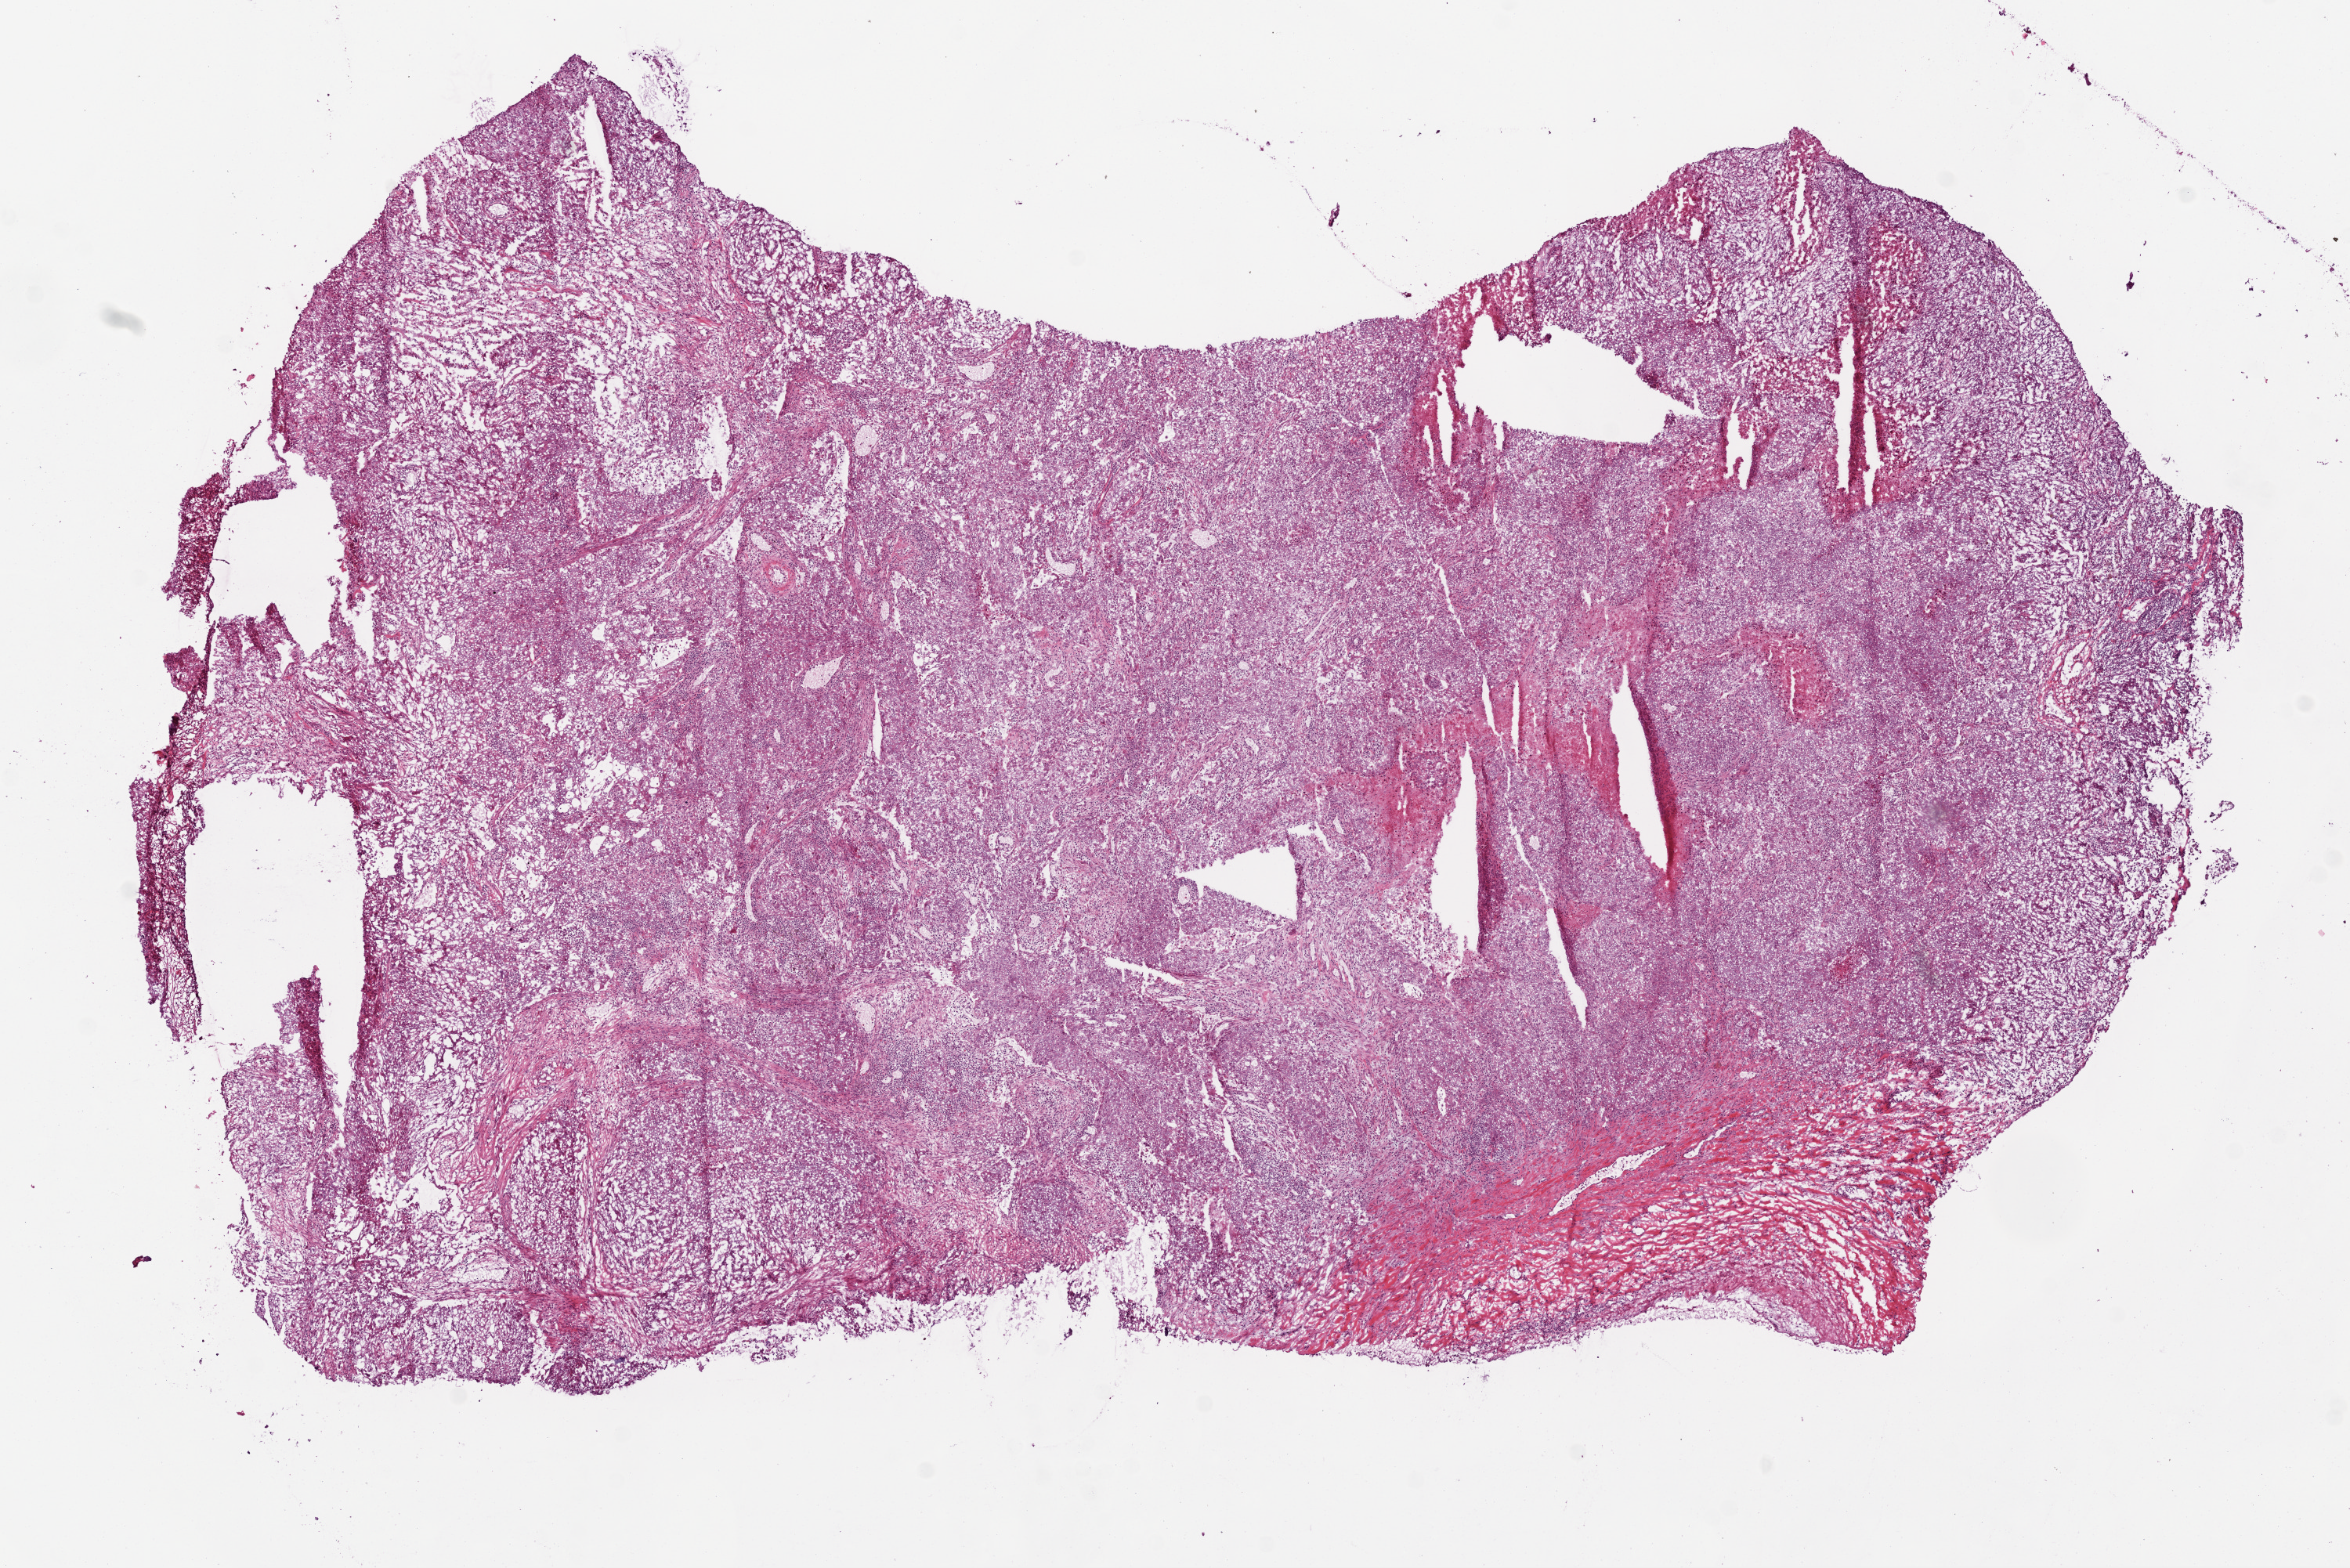
Whole-slide histology image, H&E — shown as a low-resolution overview of the whole scanned area (about 12.0 x 8.0 mm); frozen section from the bottom of the tissue portion; lung, primary tumour sample. Male patient; age at initial diagnosis 38 years. Slide review estimates, as recorded: tumour cells 70%, tumour nuclei 75%, normal cells 2%, stromal cells 20%, necrosis 8%.
- AJCC pathologic stage: IA (7th edition)
- pathologic diagnosis: Adenocarcinoma, NOS (upper lobe, lung)
- TNM: T1 N0 M0